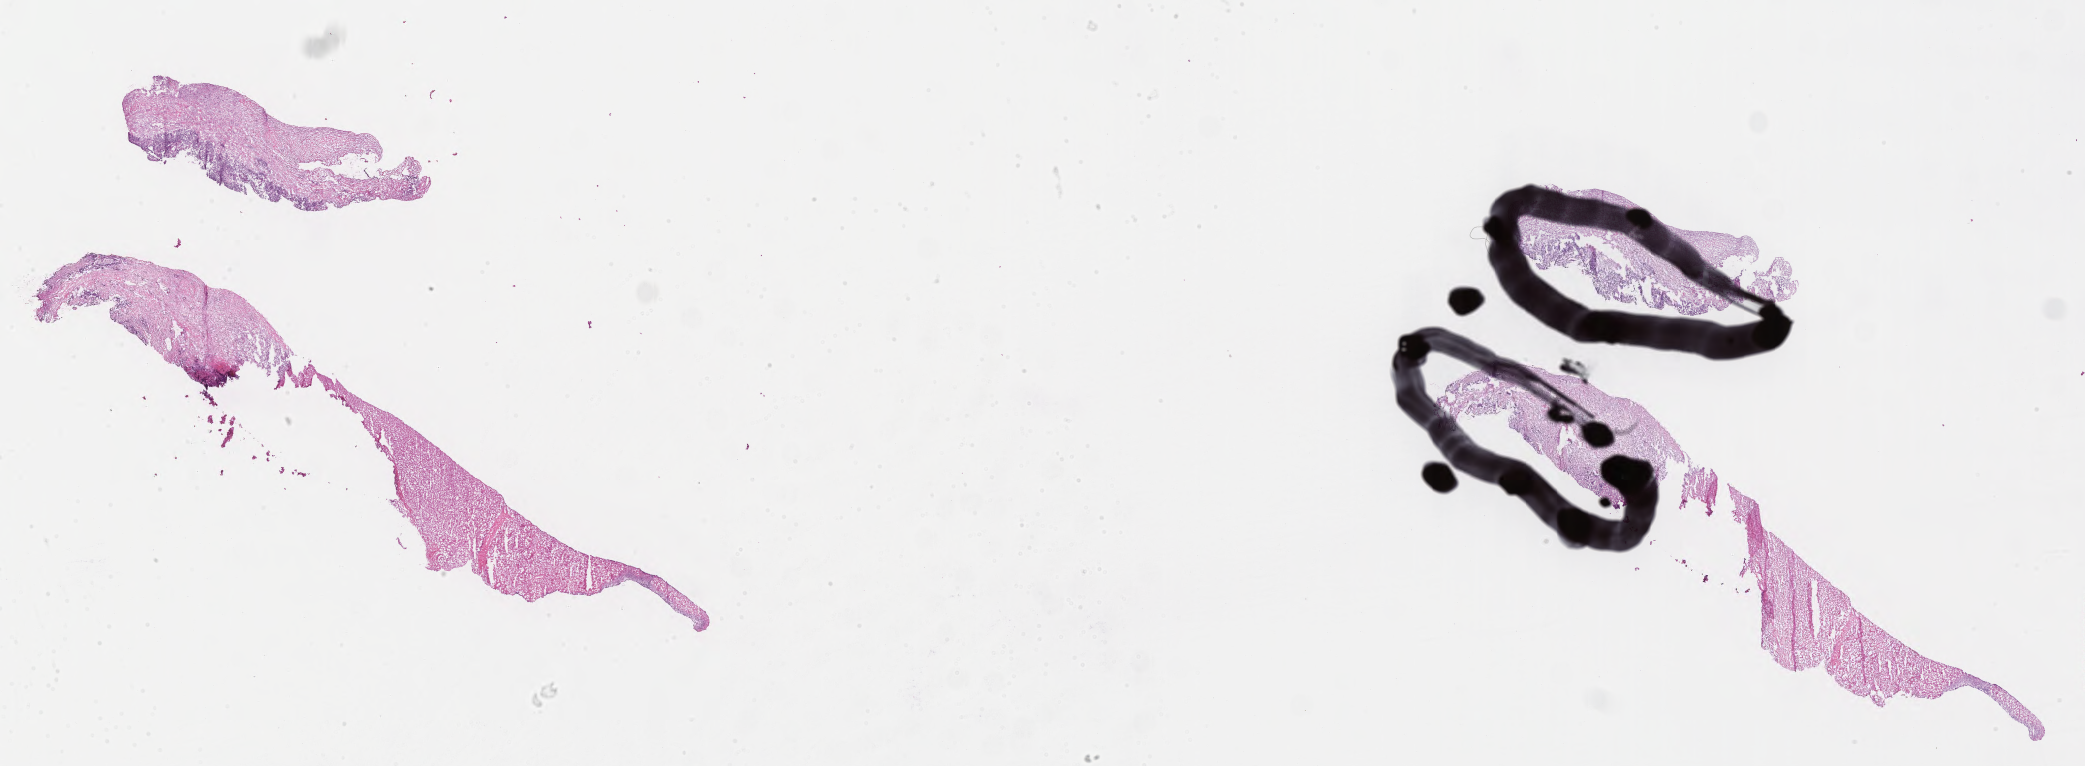
Whole-slide image, hematoxylin and eosin (H&E) stain of tumor tissue from the pelvis, low-resolution overview of the scanned area, about 33.7 x 12.4 mm, frozen section (OCT-embedded). Patient female; age 207 months (17 years 3 months).
Diagnosis (ICD-O-3 morphology term): Ewing sarcoma.